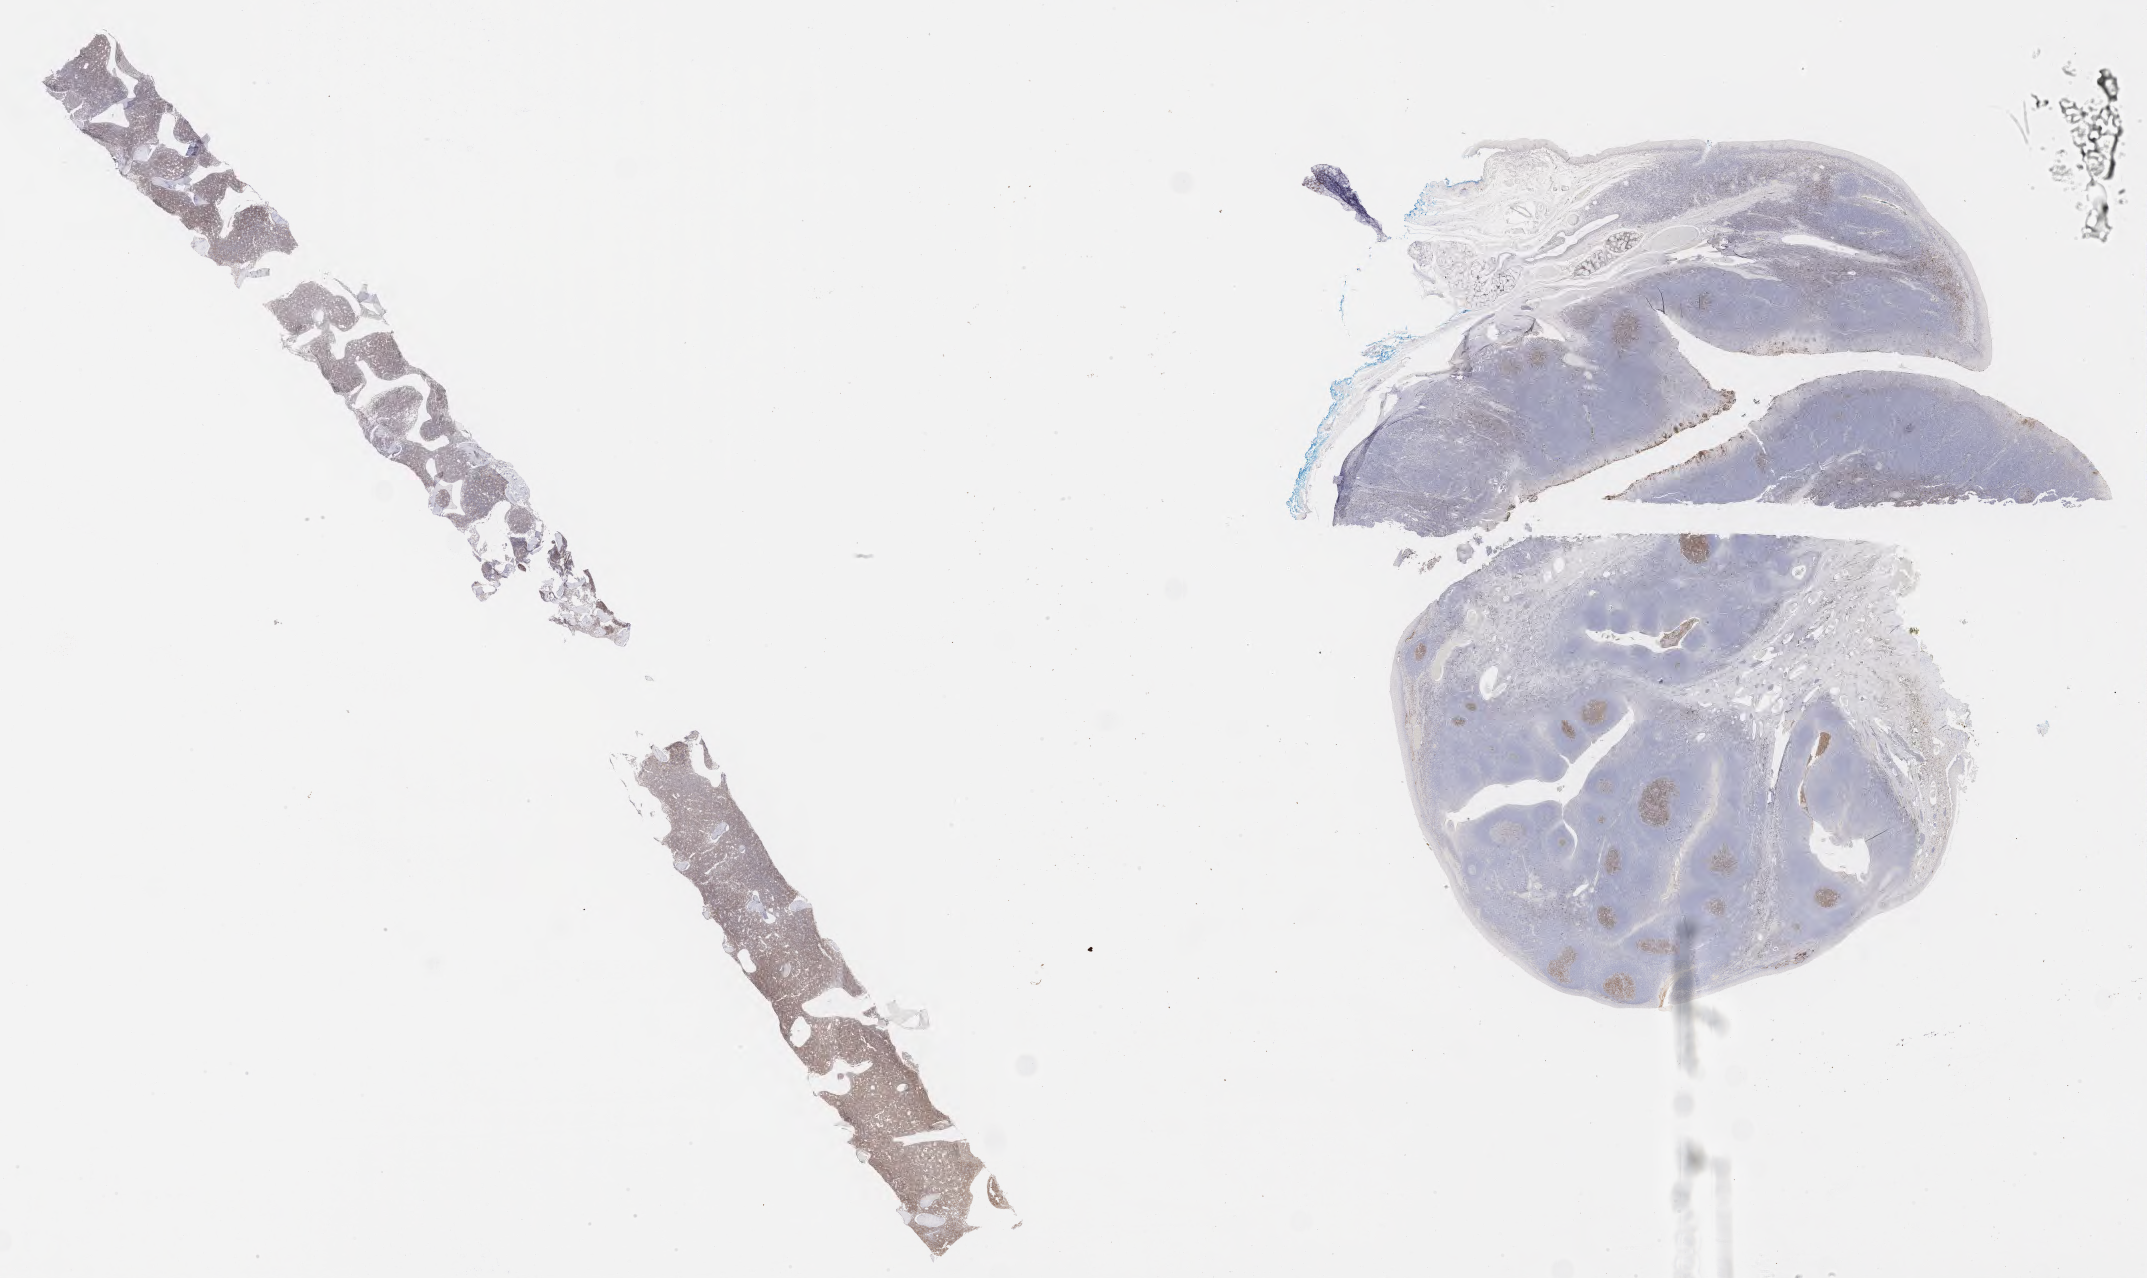
Immunohistochemistry (IHC) whole-slide image stained for CD10 — whole scanned area (about 34.7 x 20.7 mm) shown as a low-resolution overview. Specimen: tumor tissue. Patient: male, age at initial diagnosis 7 years.
Histologic diagnosis: Burkitt lymphoma, NOS.